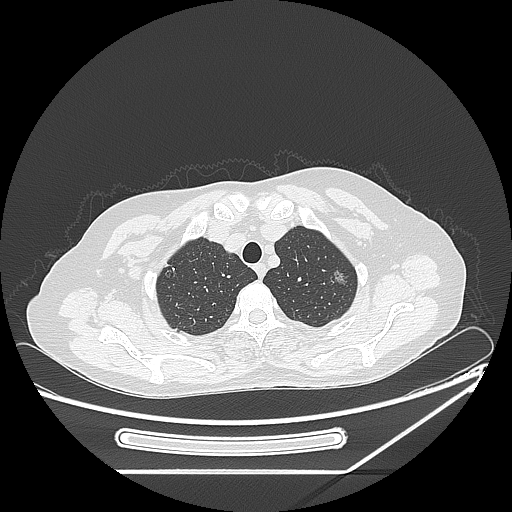
Chest CT, one axial slice. Slice 206 of 250 in the series (ordered by position). Reconstruction kernel LUNG. 120 kVp. Lung window (W 1500 / L -600 HU). 1.25 mm slice thickness. 512 × 512 image matrix. Patient: female, 57 years. Case-level facts recorded for this patient, not image findings: clinical TNM (as recorded): T1c N0 M0; histopathological grade: G2-3.
Annotated regions visible in this slice (bounding box drawn by a radiologist):
- lung tumour (recorded histology: adenocarcinoma): bounding box (x1, y1, x2, y2) in pixels: (329, 268, 348, 289)